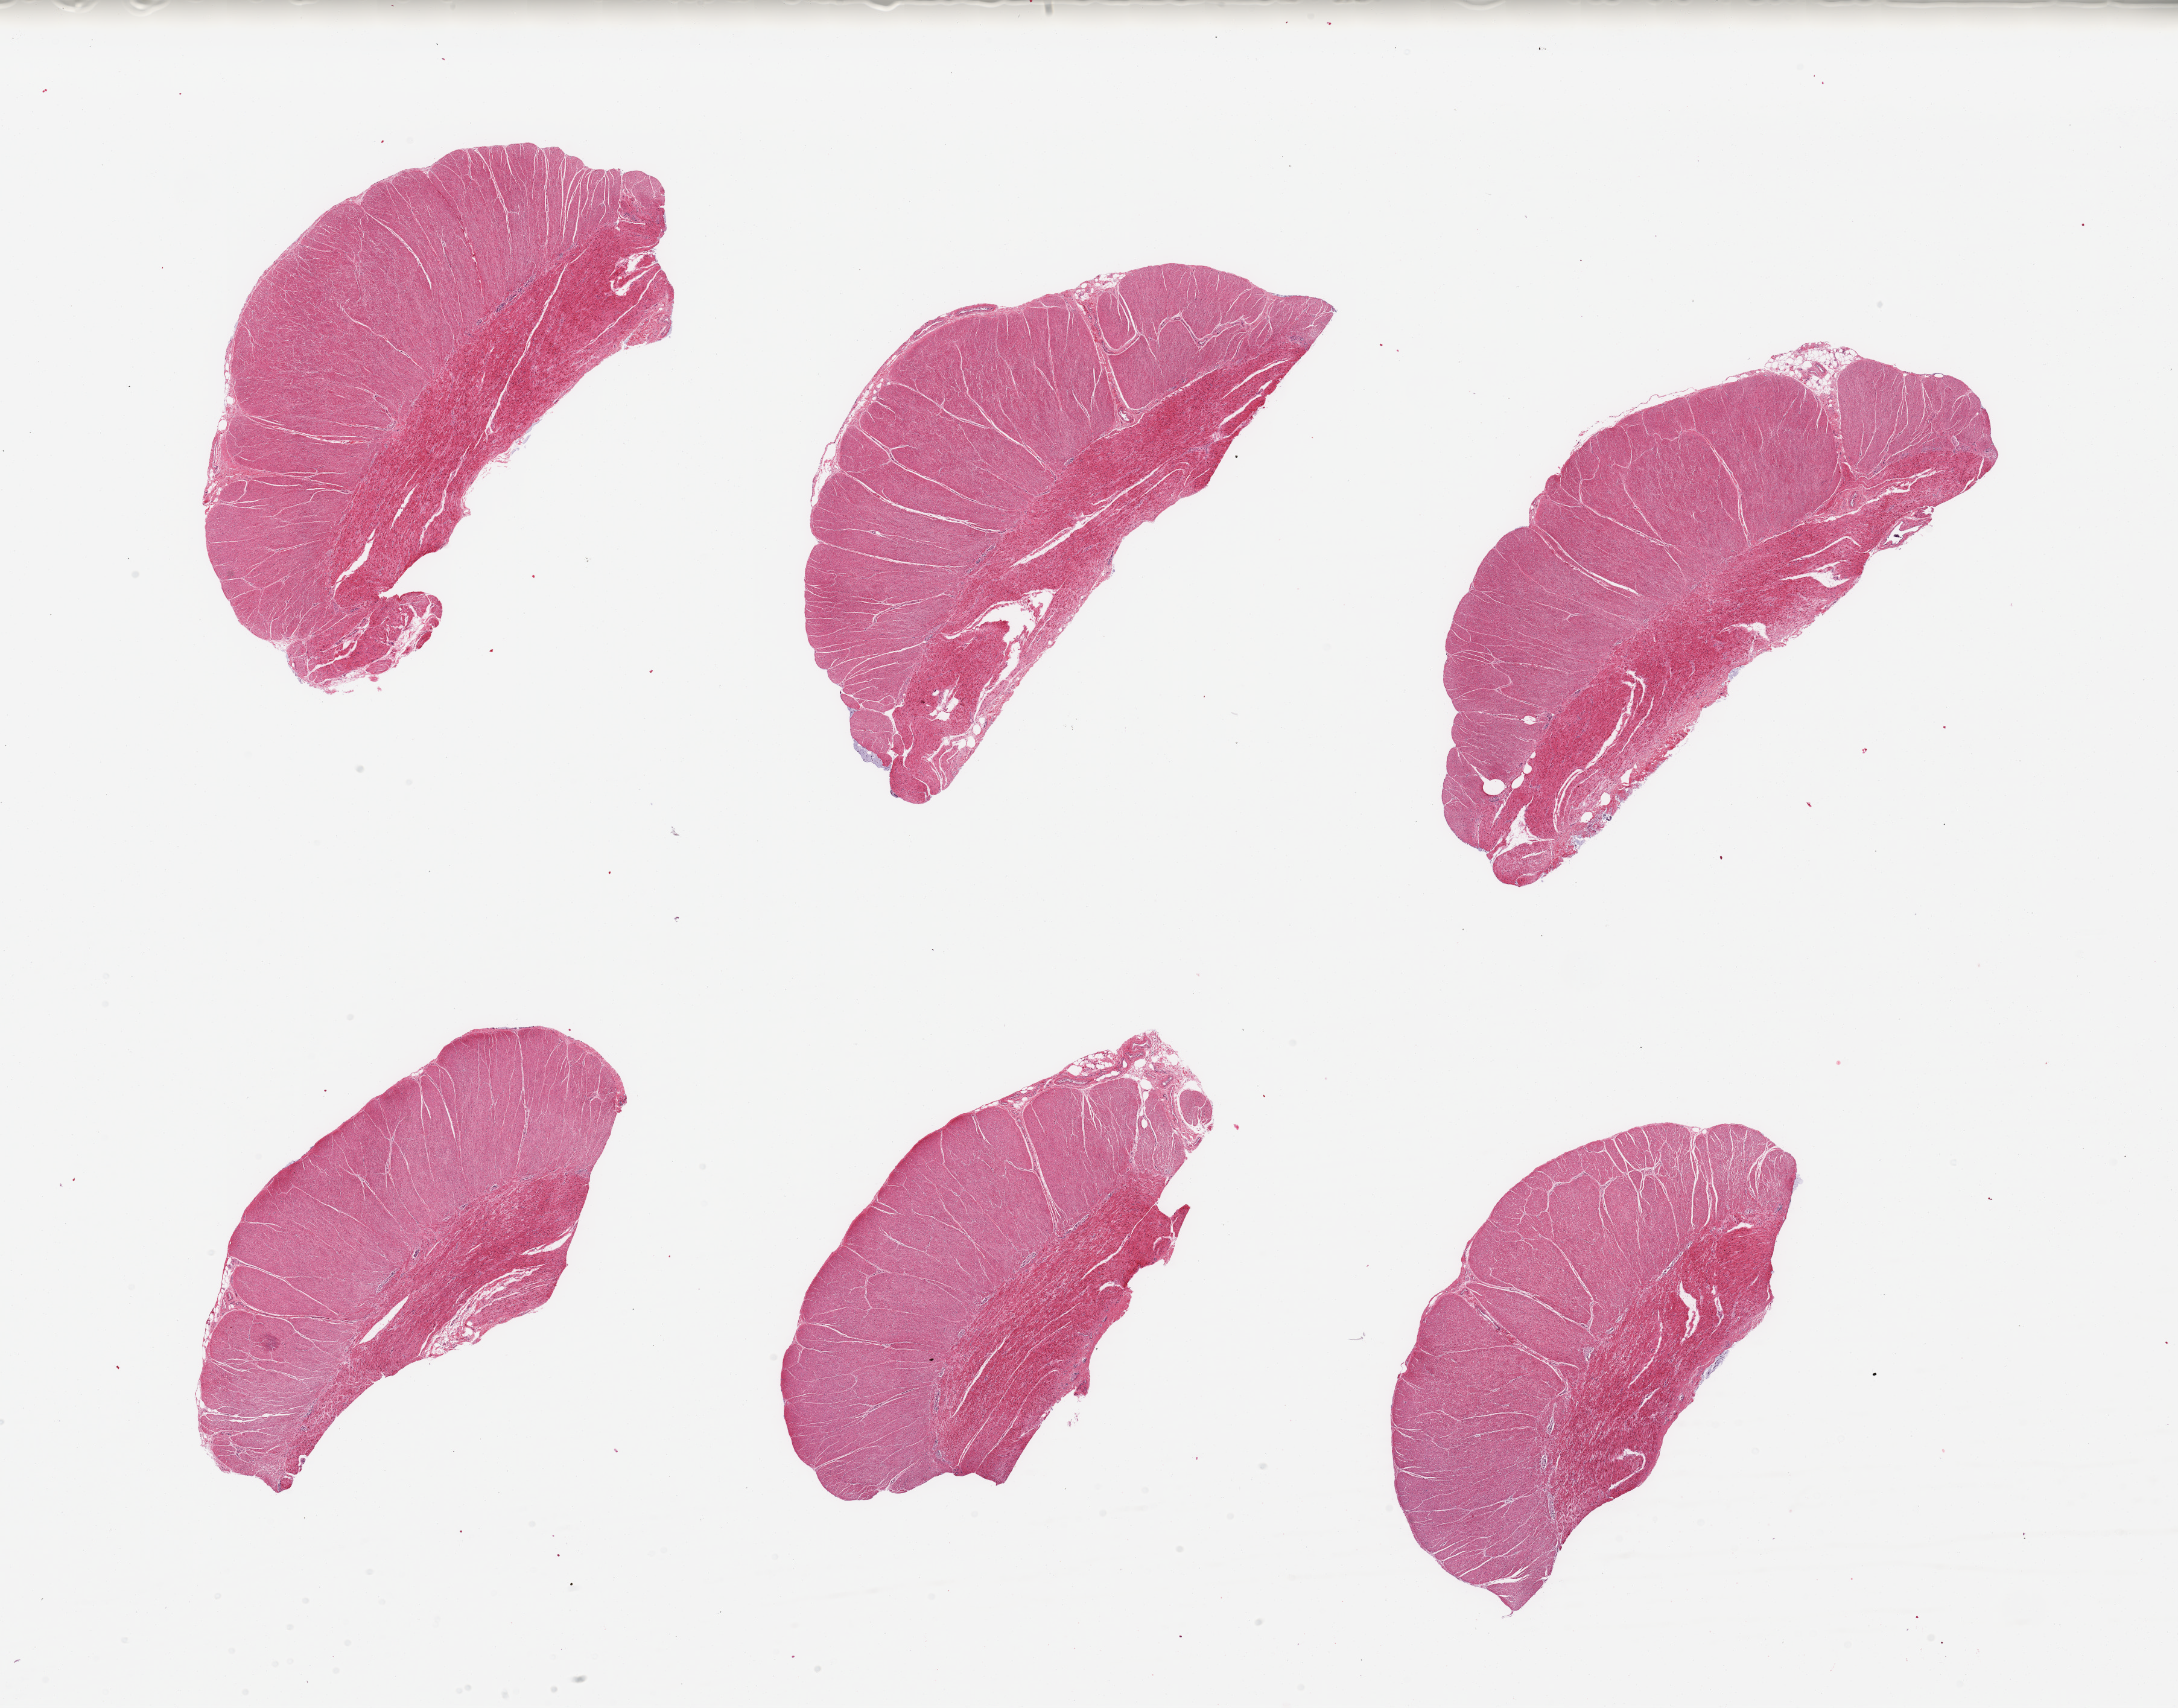
Whole-slide image, haematoxylin and eosin stain — shown as a low-resolution overview of the whole scanned area (about 28.5 x 22.4 mm, slide scanned at 20x). PAXgene-fixed paraffin-embedded (PFPE) section. Section of sigmoid colon (target tissue). Tissue donor sample.
Review note (as recorded): 6 pieces; well dissected muscularis propria.